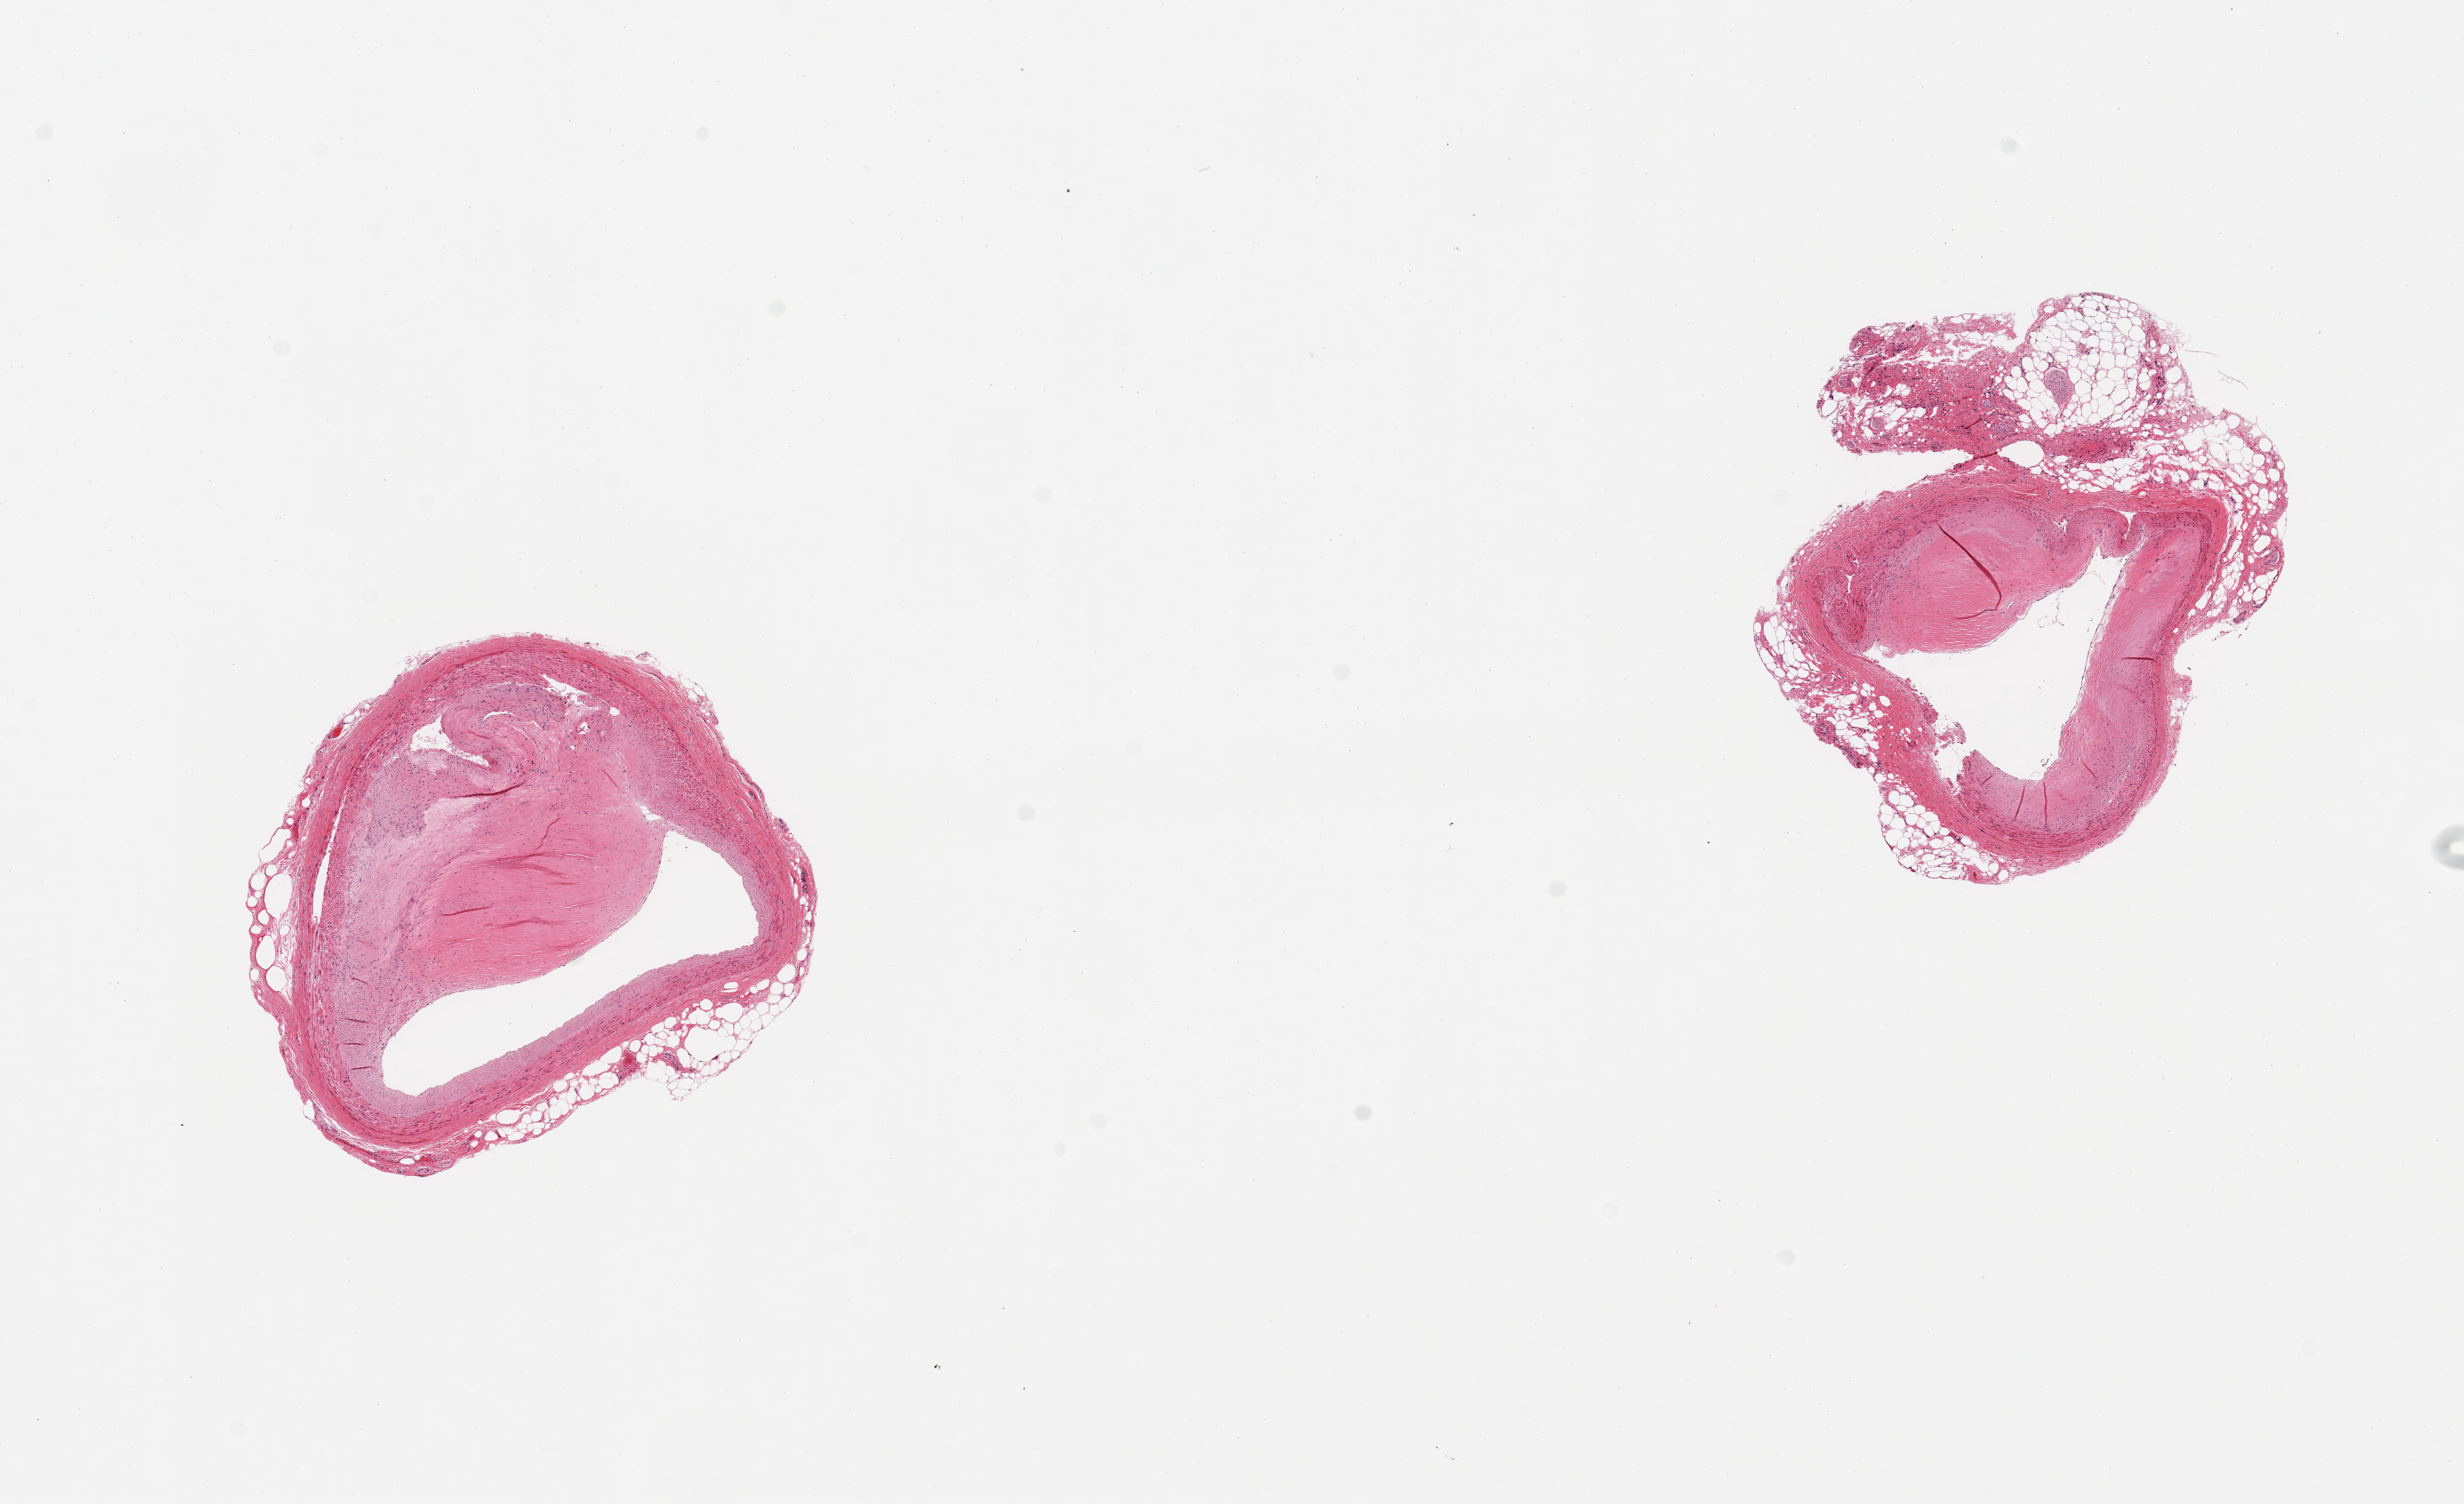
H&E whole-slide image — low-resolution overview of the scanned area, about 13.8 x 8.4 mm, PAXgene-fixed paraffin-embedded (PFPE) section, sampled site (target tissue): coronary artery, tissue donor sample. Donor sex: male.
Pathologist's review note for this sample: 2 pieces, atheromatous occlusion up to ~80%, adherent nubbin of fat, ~1mm.